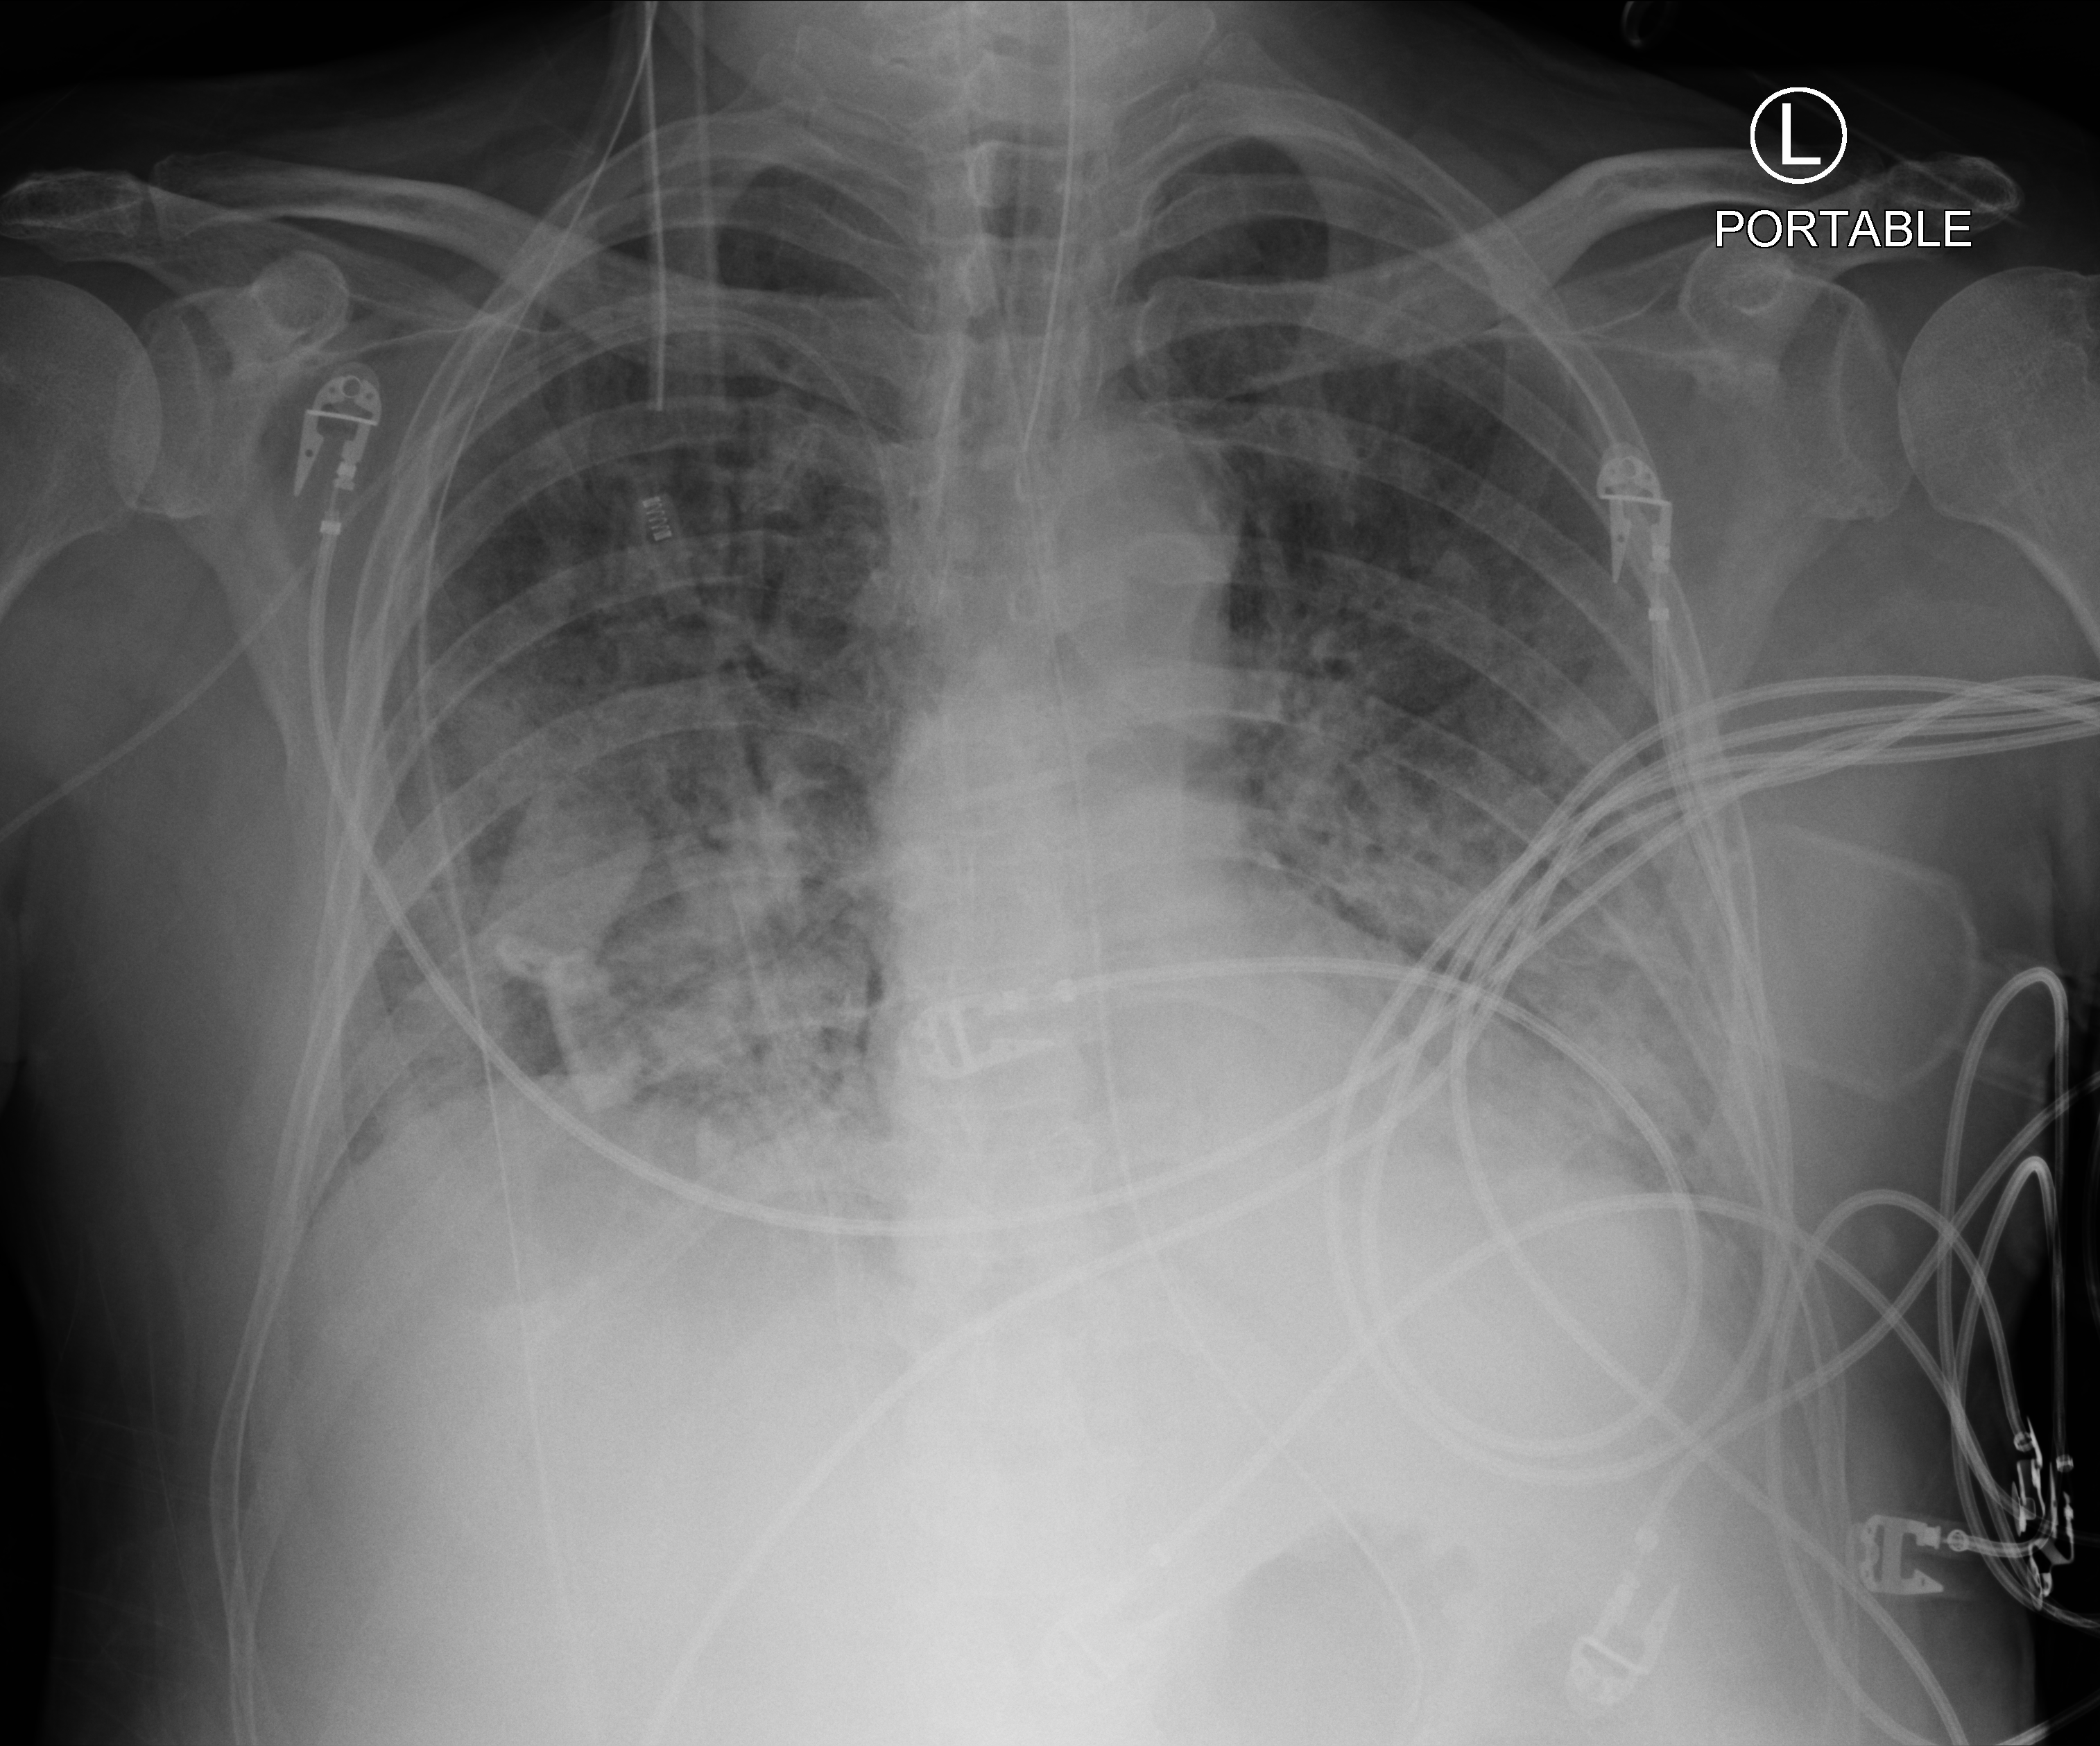
Portable chest radiograph, anteroposterior (AP) projection. Male patient hospitalised with COVID-19, age 60–74 years.
Admission-level facts for this patient (not findings on this image; timing relative to this image not recorded): admitted to intensive care during this hospital stay: yes.